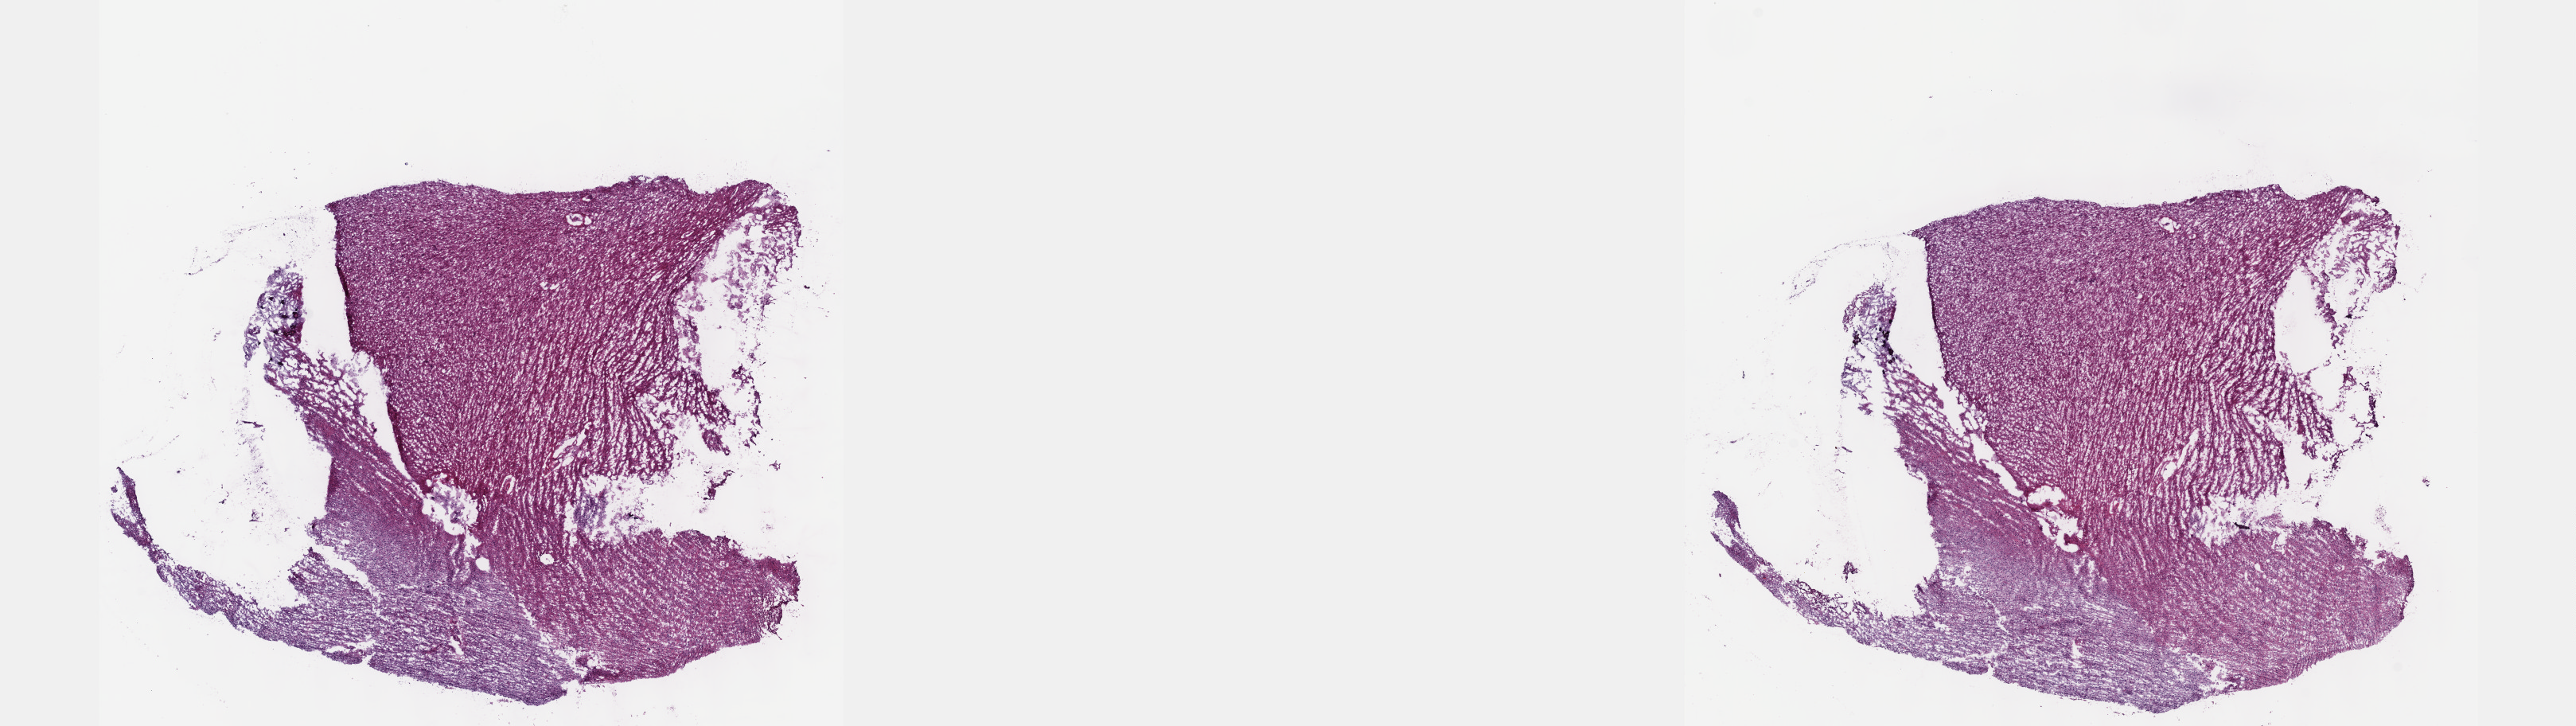
Hematoxylin and eosin (H&E) stained whole-slide image — shown as a low-resolution overview of the whole scanned area (about 26.2 x 7.4 mm, slide scanned at 40x); frozen section from the top of the tissue portion; brain, primary tumour sample. Male, age 36 years at initial diagnosis. Histologic grade: G3 (poorly differentiated). Pathologist review of this section (percent, as recorded): tumour cells 55%, tumour nuclei 90%, normal cells 10%, stromal cells 35%, necrosis 0%. Infiltration values recorded for this section: lymphocyte infiltration 0%, monocyte infiltration 0%, neutrophil infiltration 0%.
Histologic diagnosis: Oligodendroglioma, anaplastic (cerebrum).